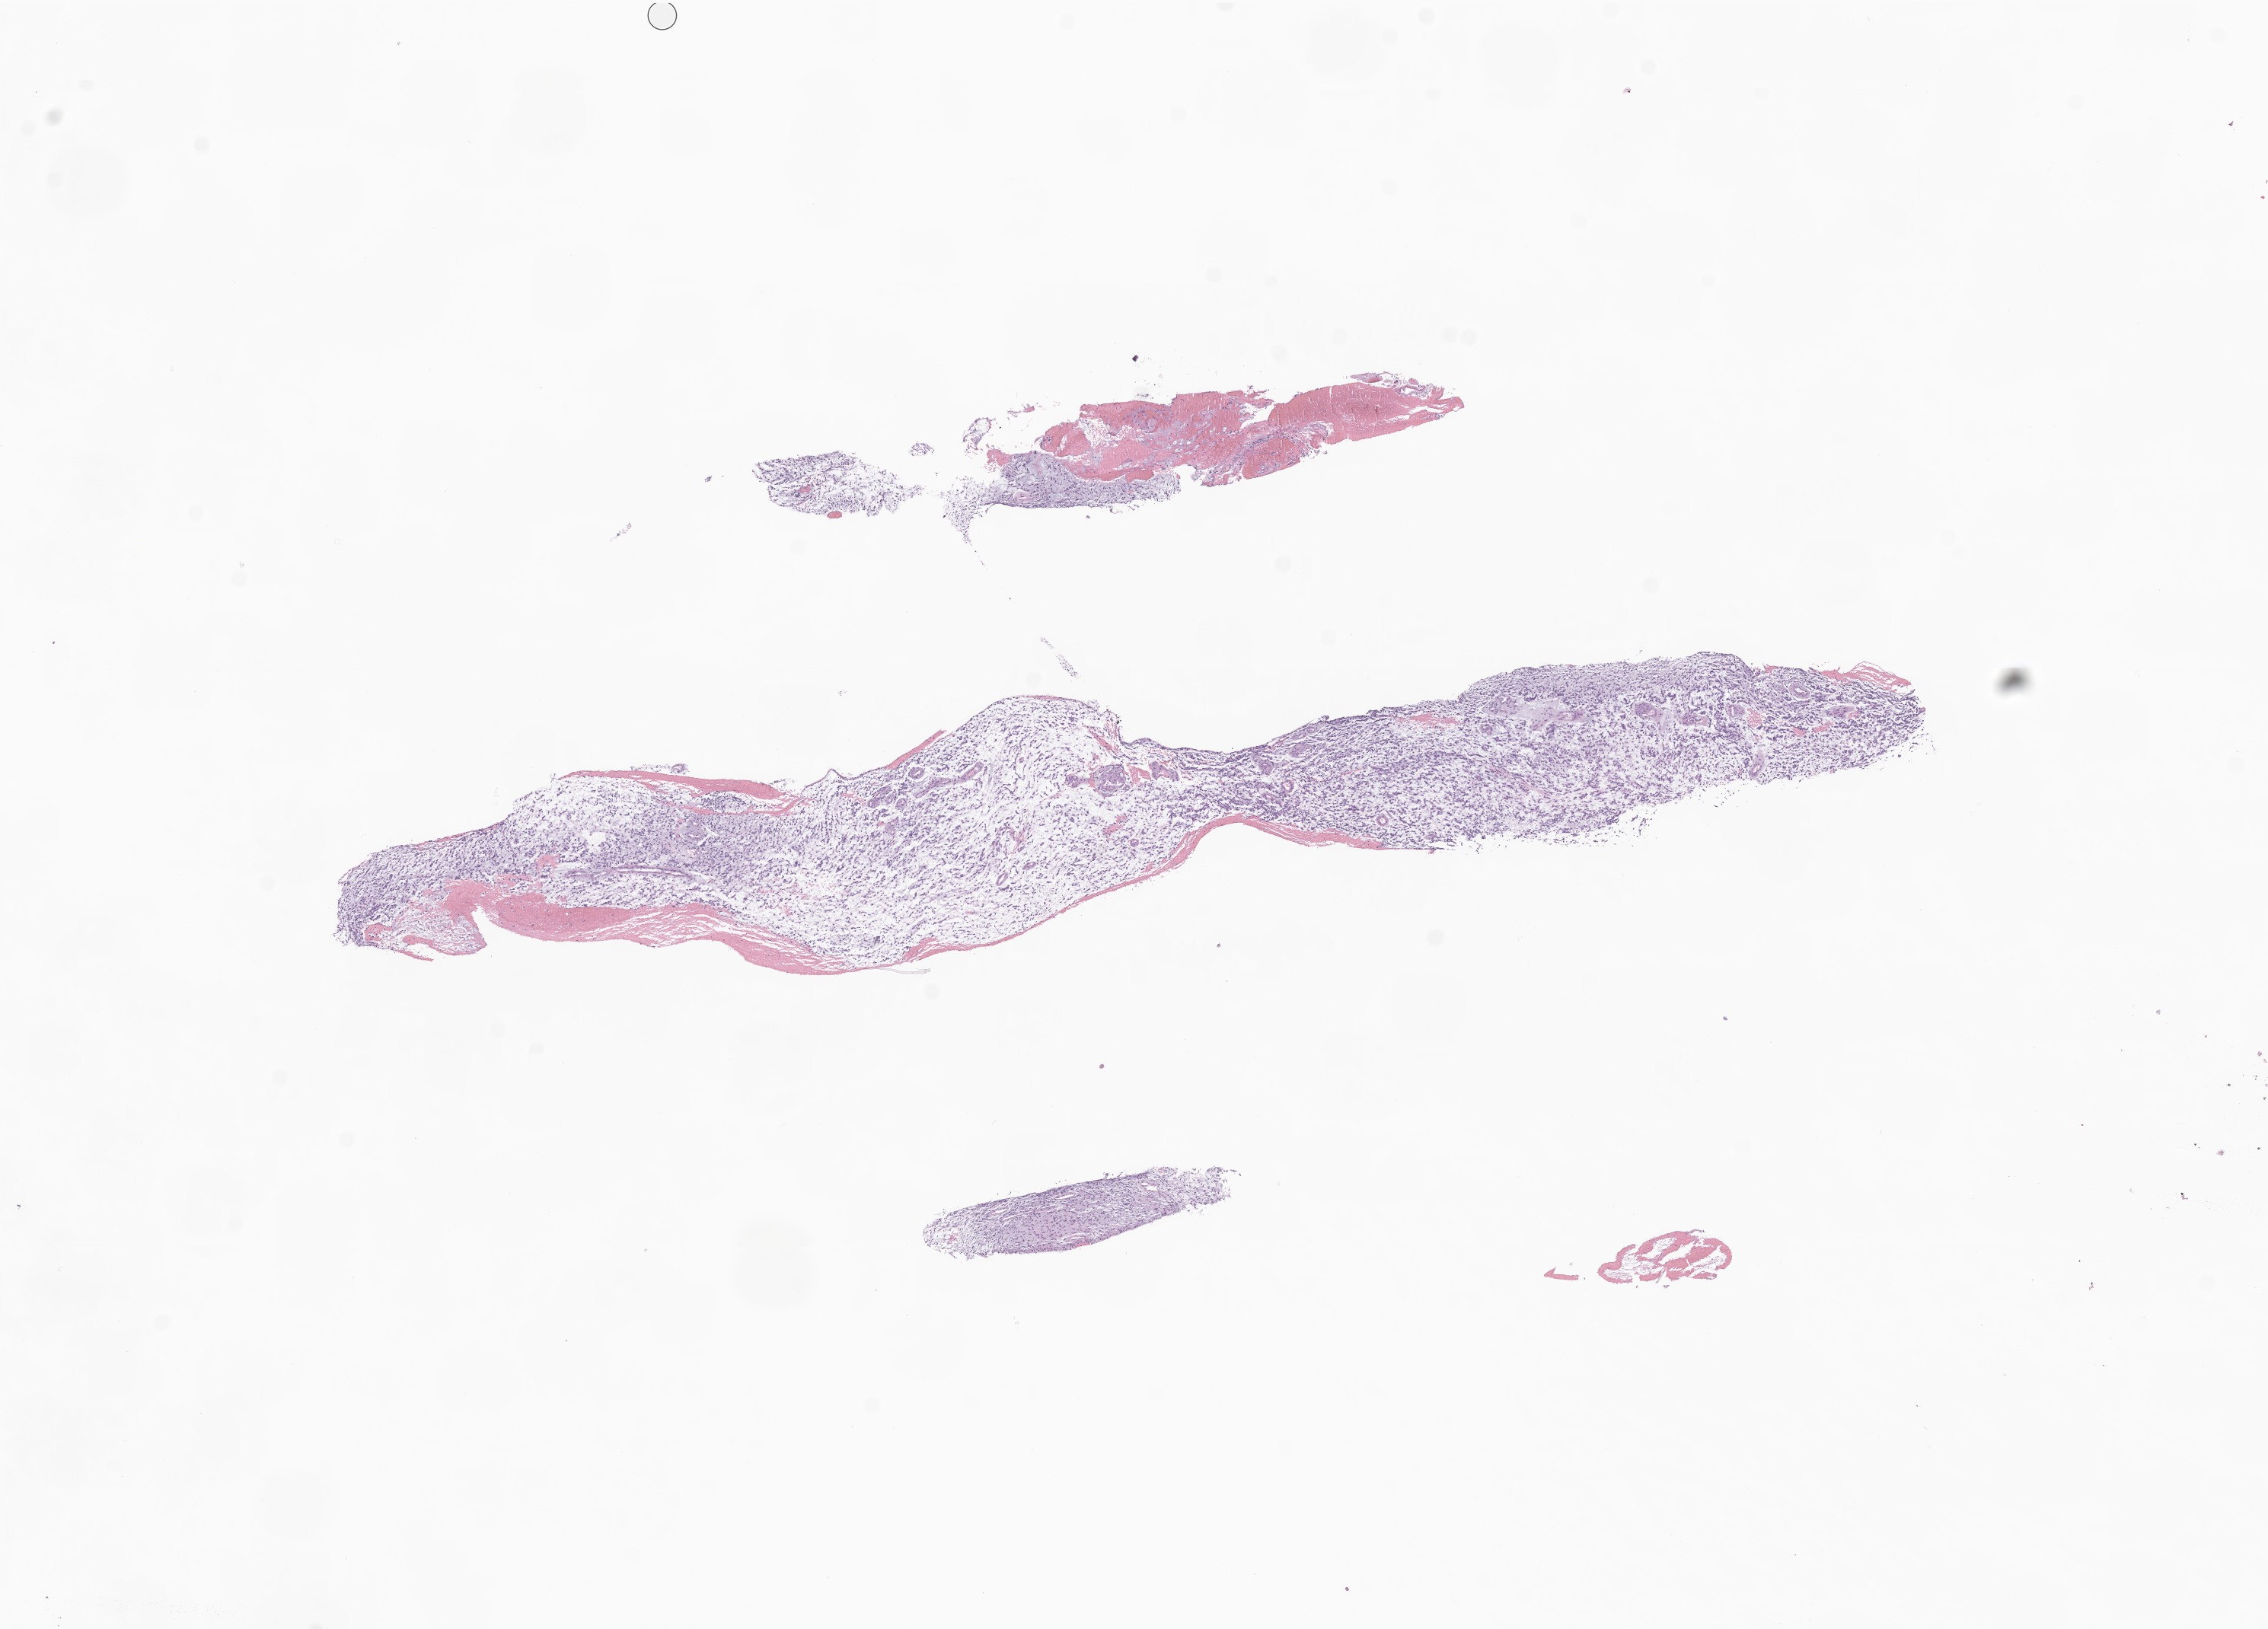
Hematoxylin and eosin (H&E) whole-slide image of tumor tissue from the brain — a low-resolution overview of the entire scanned area, about 12.6 x 9.0 mm; formalin-fixed paraffin-embedded section. Male patient, age 79 months (6 years 7 months).
Recorded diagnosis: Glioma, malignant.